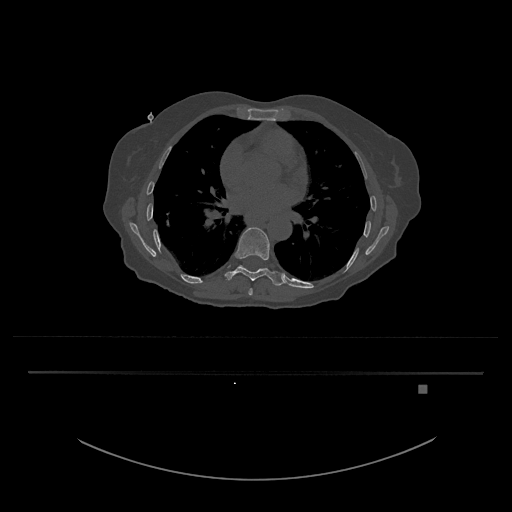
CT including the spine, one axial slice. Slice 758 of 797 in the series (ordered by position). Bone window (W 1800 / L 400 HU). 0.5 mm slice thickness. 512 × 512 image matrix, field of view 500 × 500 mm. Patient: female, 57 years. Case-level facts recorded for this patient, not image findings: primary cancer: cervical.
Outlined on this slice (semi-automatic segmentation, software-assisted and operator-edited):
- T10 vertebra: bounding box <239,265,266,272> (left, top, right, bottom; pixels)
- T8 vertebra: <248,288,253,296>
- T9 vertebra: <225,227,284,286>